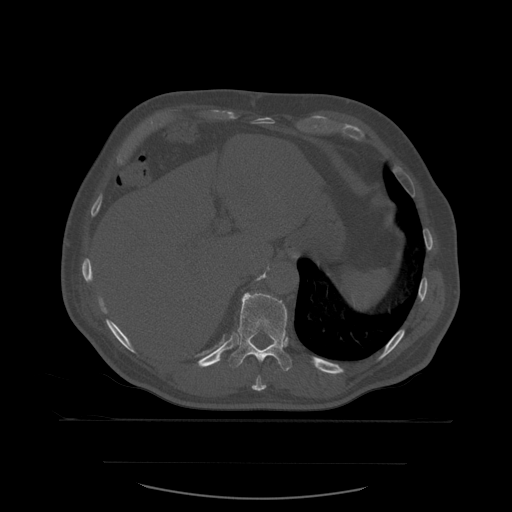
CT including the spine, one axial slice; position 299 of 590 along the scan axis; bone window (W 1800 / L 400 HU); 1.25 mm slice thickness; 512 × 512 image matrix, field of view 479 × 479 mm. Patient age 71 years. Case-level facts recorded for this patient, not image findings: primary cancer: lung; vertebrae with lytic lesions (as recorded): T1, T2, L5, S1.
Annotated regions visible in this slice (semi-automatic segmentation, software-assisted and operator-edited):
- T10 vertebra: box from (x=252, y=376) to (x=267, y=391) px
- T11 vertebra: (x=228, y=293)–(x=293, y=371)